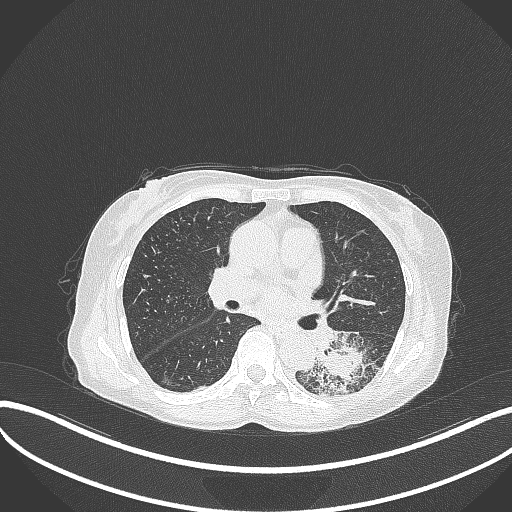
Chest CT, one axial slice. Reconstruction kernel B70f. 120 kVp. Lung window (W 1500 / L -600 HU). 1 mm slice thickness. 512 × 512 image matrix. Patient: female, 78 years. From the clinical record (not read from this slice): clinical TNM (as recorded): T3 N0 M1.
Structures marked on this image (bounding box drawn by a radiologist):
- lung tumour (recorded histology: squamous cell carcinoma): bounding box [x1, y1, x2, y2] px = [312, 324, 379, 396]